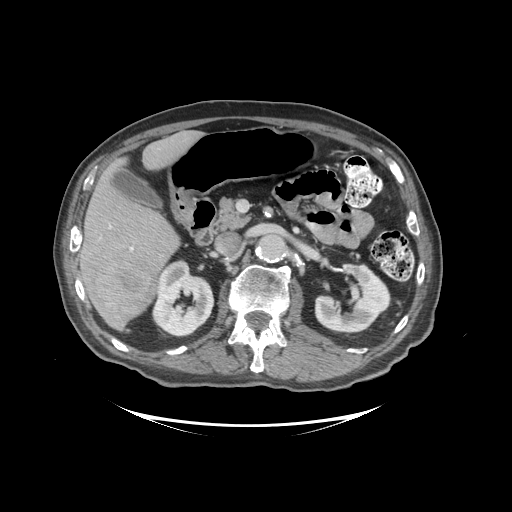
Contrast-enhanced abdominal CT (liver protocol), one axial slice; reconstruction kernel STANDARD; 140 kVp; soft-tissue window (W 400 / L 40 HU); 2.5 mm slice thickness; 512 × 512 image matrix, field of view 460 × 460 mm. From the clinical record (not read from this slice): diagnosis: hepatocellular carcinoma (patient treated with transarterial chemoembolisation; whether this scan precedes or follows treatment is not stated here); TNM stage (as recorded): Stage-I; Child-Pugh class: A; tumour differentiation: moderately differentiated; tumour nodularity: uninodular.
Annotated regions visible in this slice (semi-automatically segmented with operator editing):
- liver parenchyma outside the tumour (the mass and vessels are separate outlines, so this box may not span the whole liver): bounding box [x1, y1, x2, y2] px = [80, 130, 200, 330]
- mass: [86, 260, 157, 319]
- liver vessels: [109, 225, 133, 251]